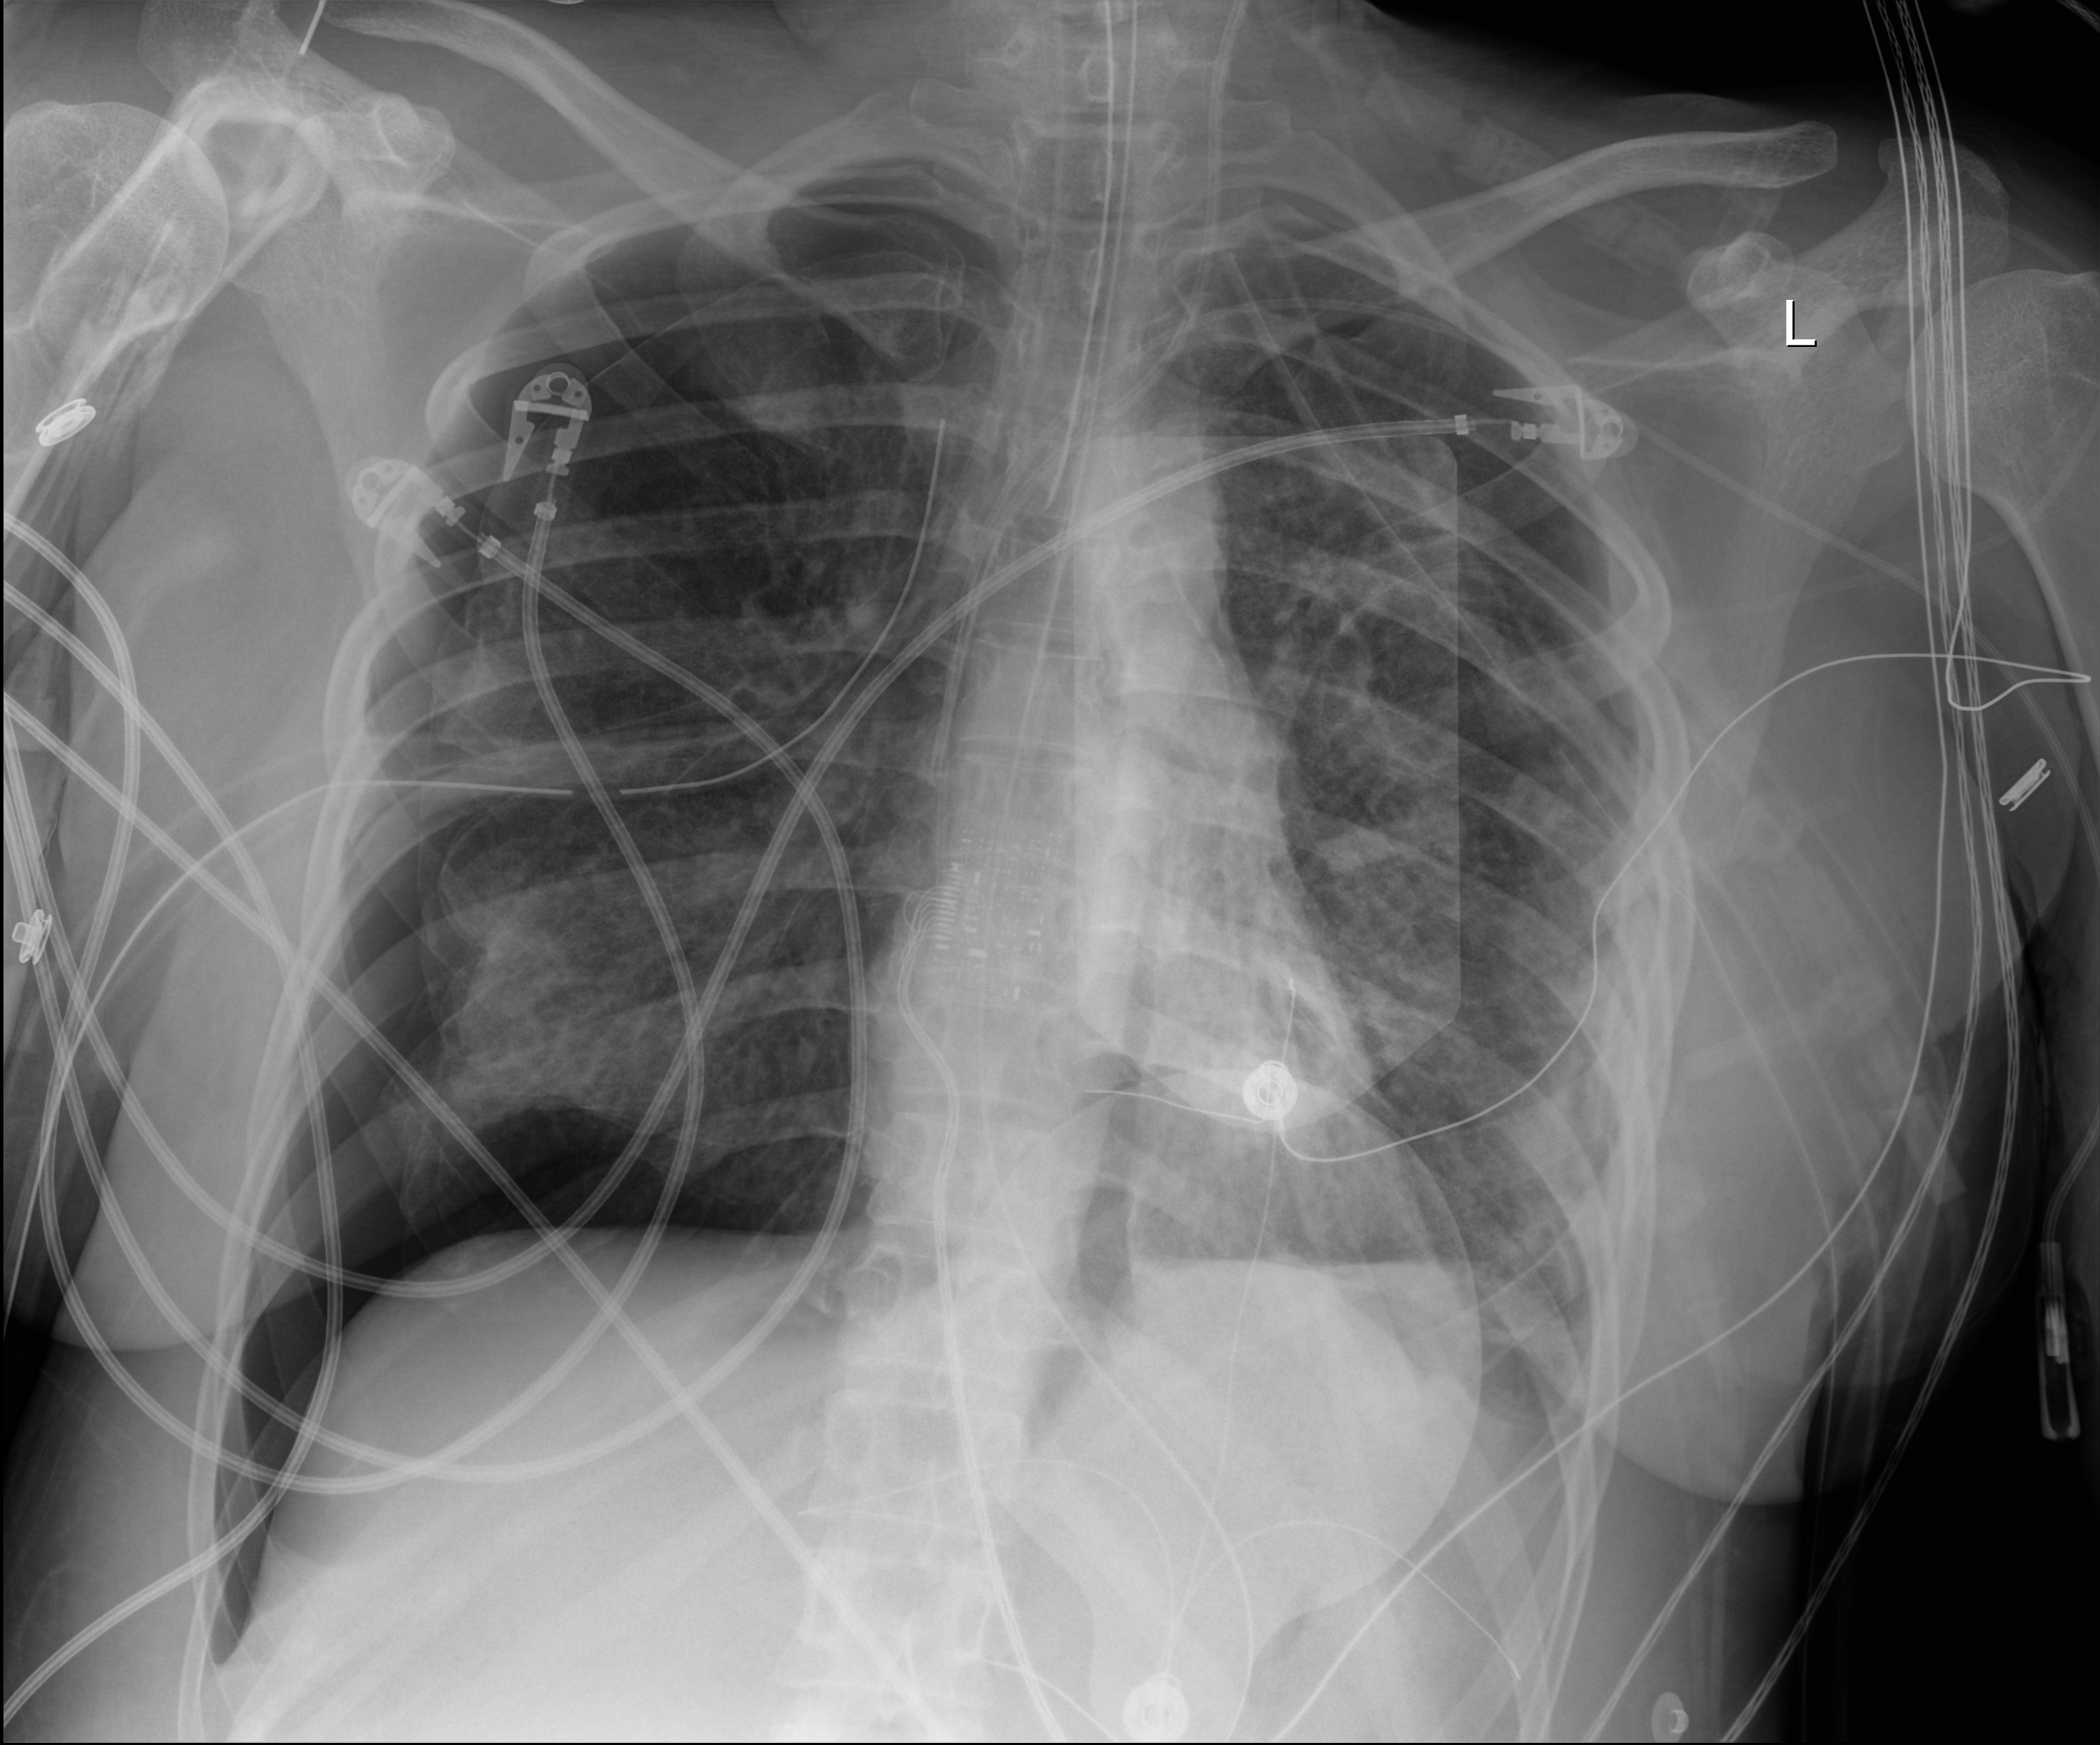
Portable chest radiograph, anteroposterior (AP) projection. Adult patient hospitalised with COVID-19, age 18–59 years.
From the hospital-stay record, not from the radiograph (when in the stay this image was taken is not recorded): hypertension (admission record): no; mechanically ventilated during this hospital stay: yes; admitted to intensive care during this hospital stay: yes.